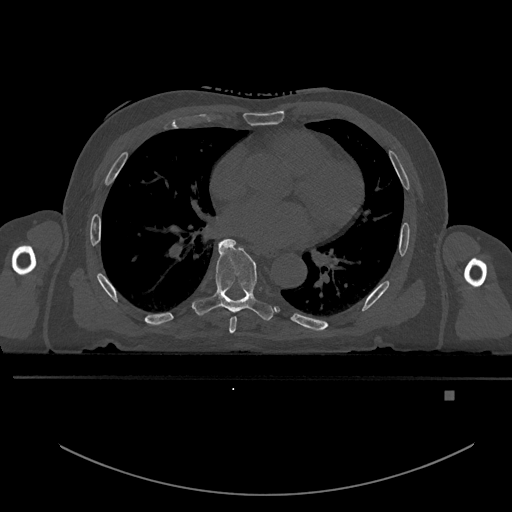
CT including the spine, one axial slice. Position 261 of 969 along the scan axis. Bone window (W 1800 / L 400 HU). 0.5 mm slice thickness. 512 × 512 image matrix, field of view 456 × 456 mm. Patient: male, 82 years. Case-level facts recorded for this patient, not image findings: primary cancer: prostate.
Structures marked on this image (semi-automatically segmented with operator editing):
- T6 vertebra: bounding box <229,316,237,334> (left, top, right, bottom; pixels)
- T7 vertebra: <192,238,273,321>